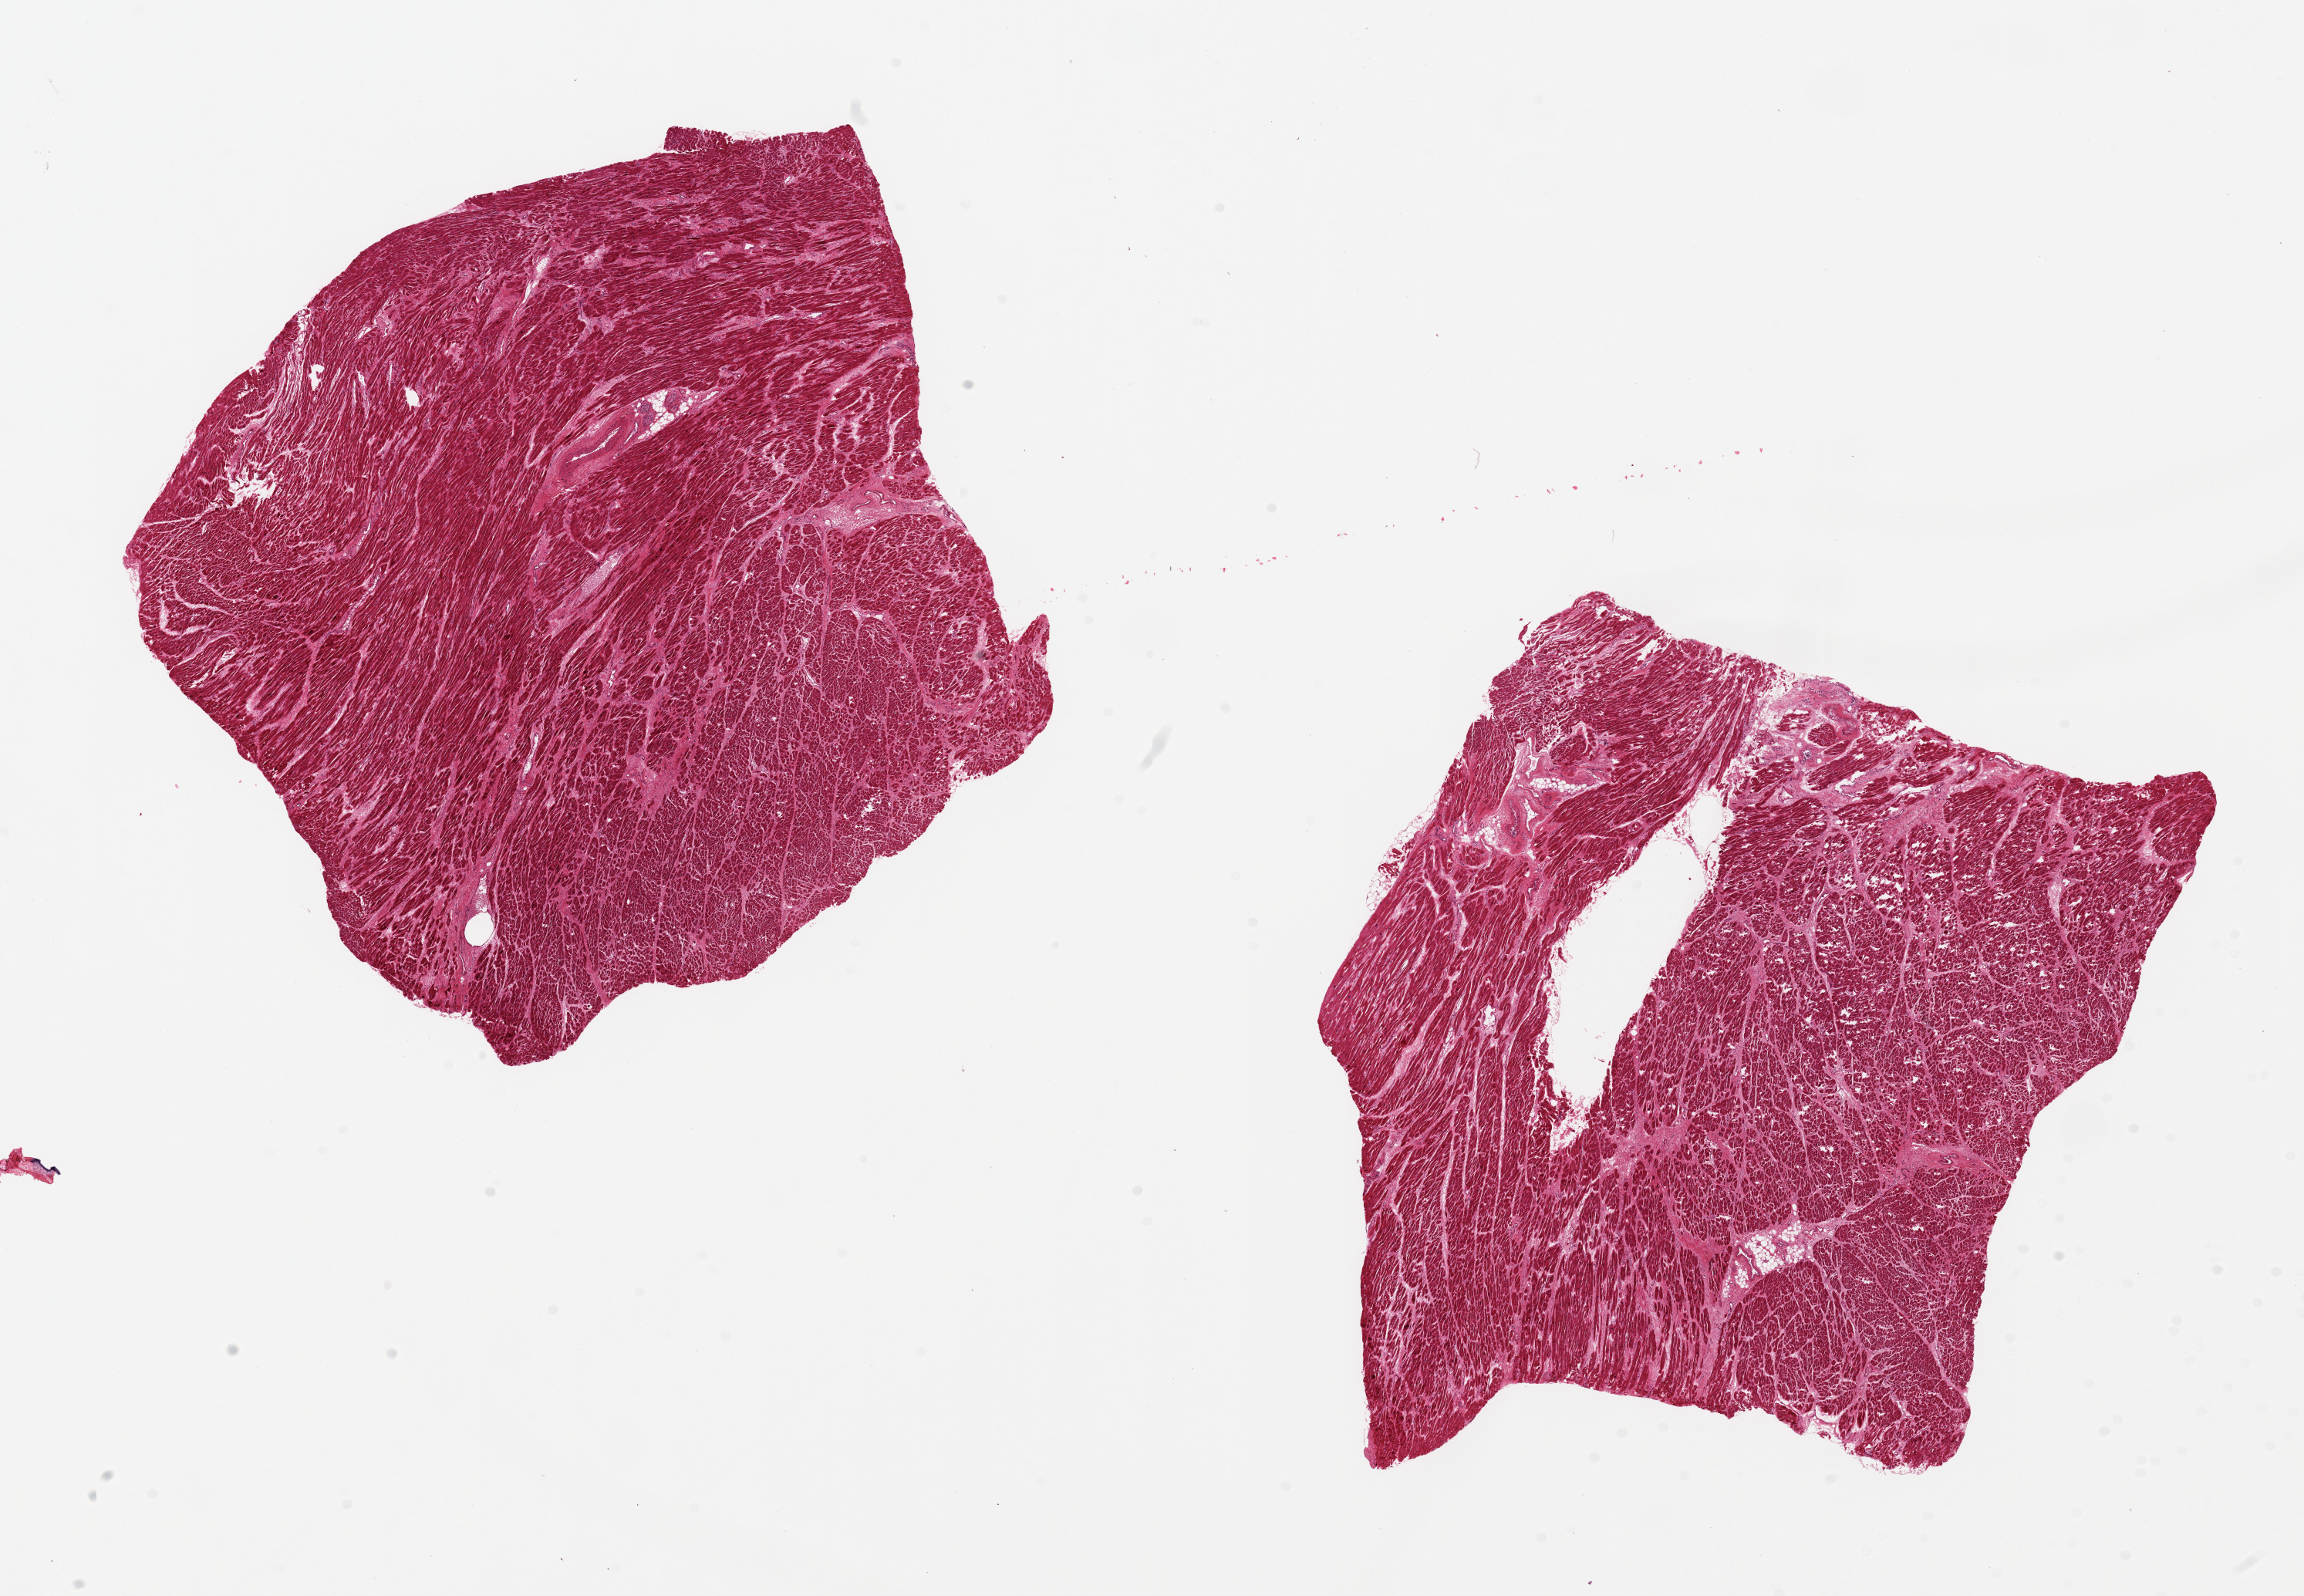
Whole-slide image, H&E stain — low-resolution overview of the scanned area, about 23.6 x 16.4 mm, PAXgene-fixed, paraffin-embedded tissue, target tissue: heart, tissue donor sample. Male donor.
Pathologist's review note for this sample: 2 pieces, 9x8 & 9x7mm; patchy fibrosis probably from old ischemia.